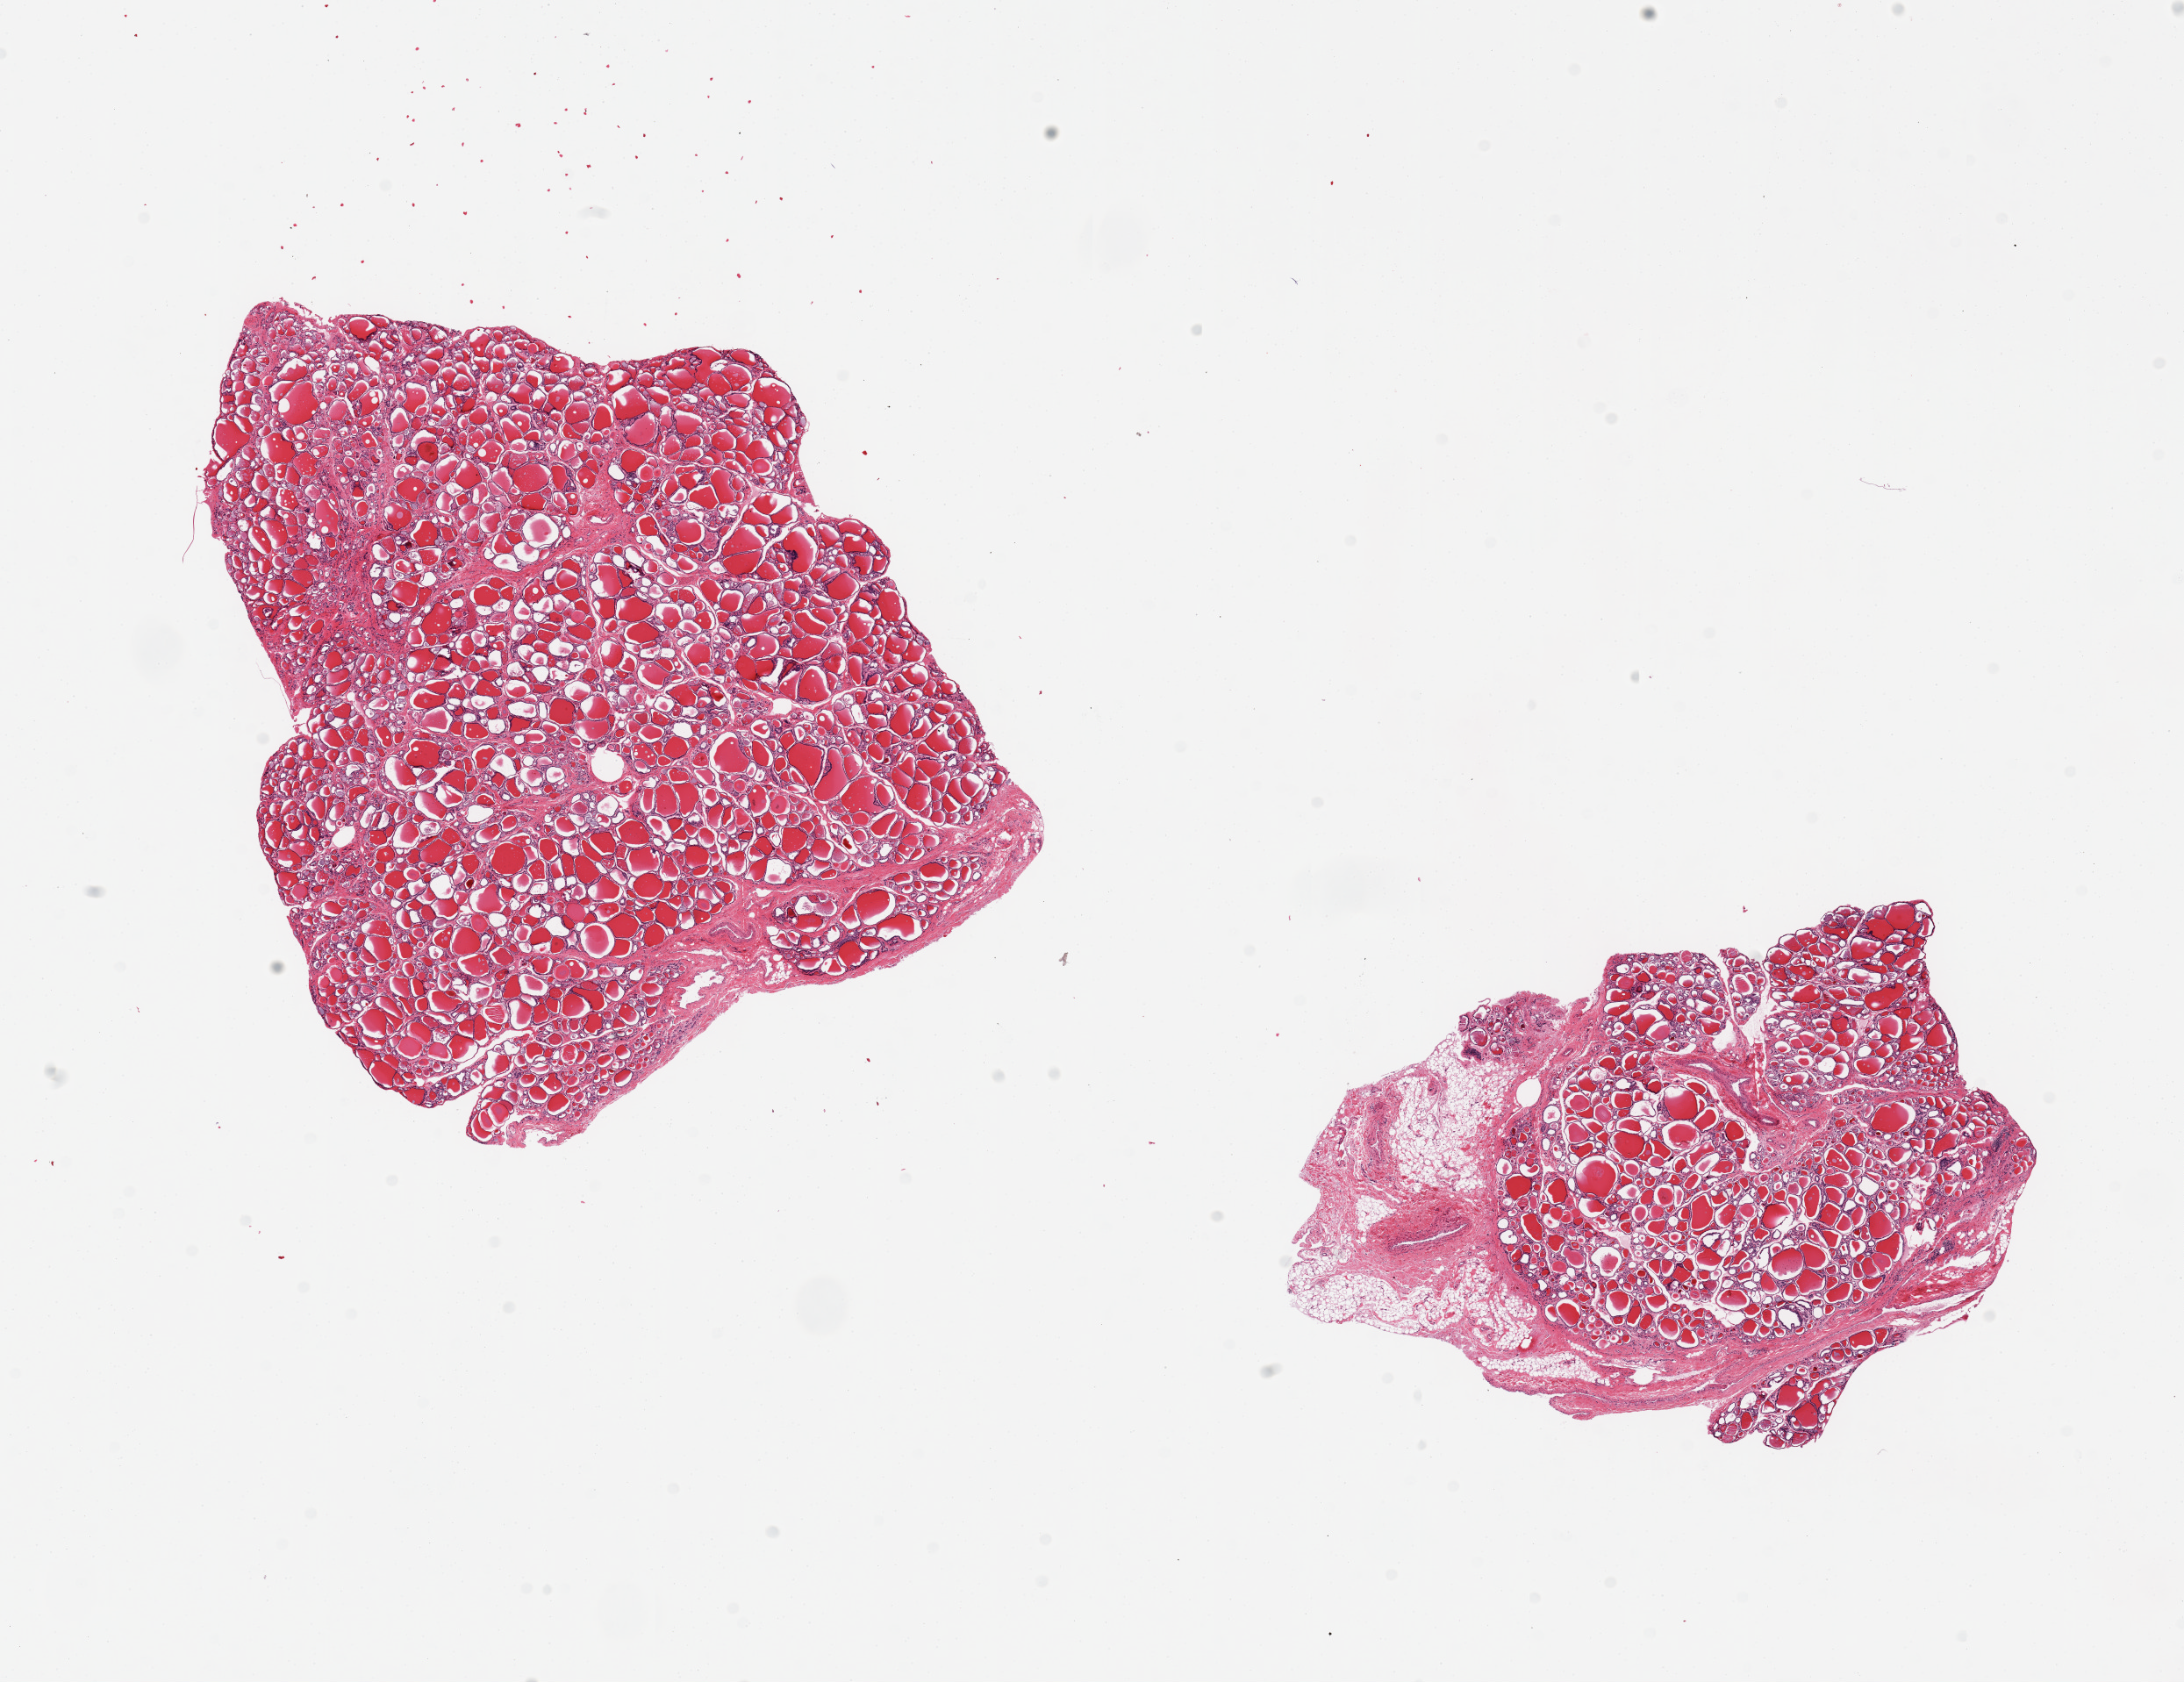
Digitized hematoxylin and eosin (H&E)-stained section — a low-resolution overview of the entire scanned area, about 19.7 x 15.2 mm (acquisition: 20x scan). PAXgene-fixed, paraffin-embedded tissue. Sampled site (target tissue): thyroid. Donor tissue sample. Donor: male.
Pathologist's review note for this sample: 2 pieces, slight nodularity/fibrosis, smaller piece is ~30% fat and vessels.